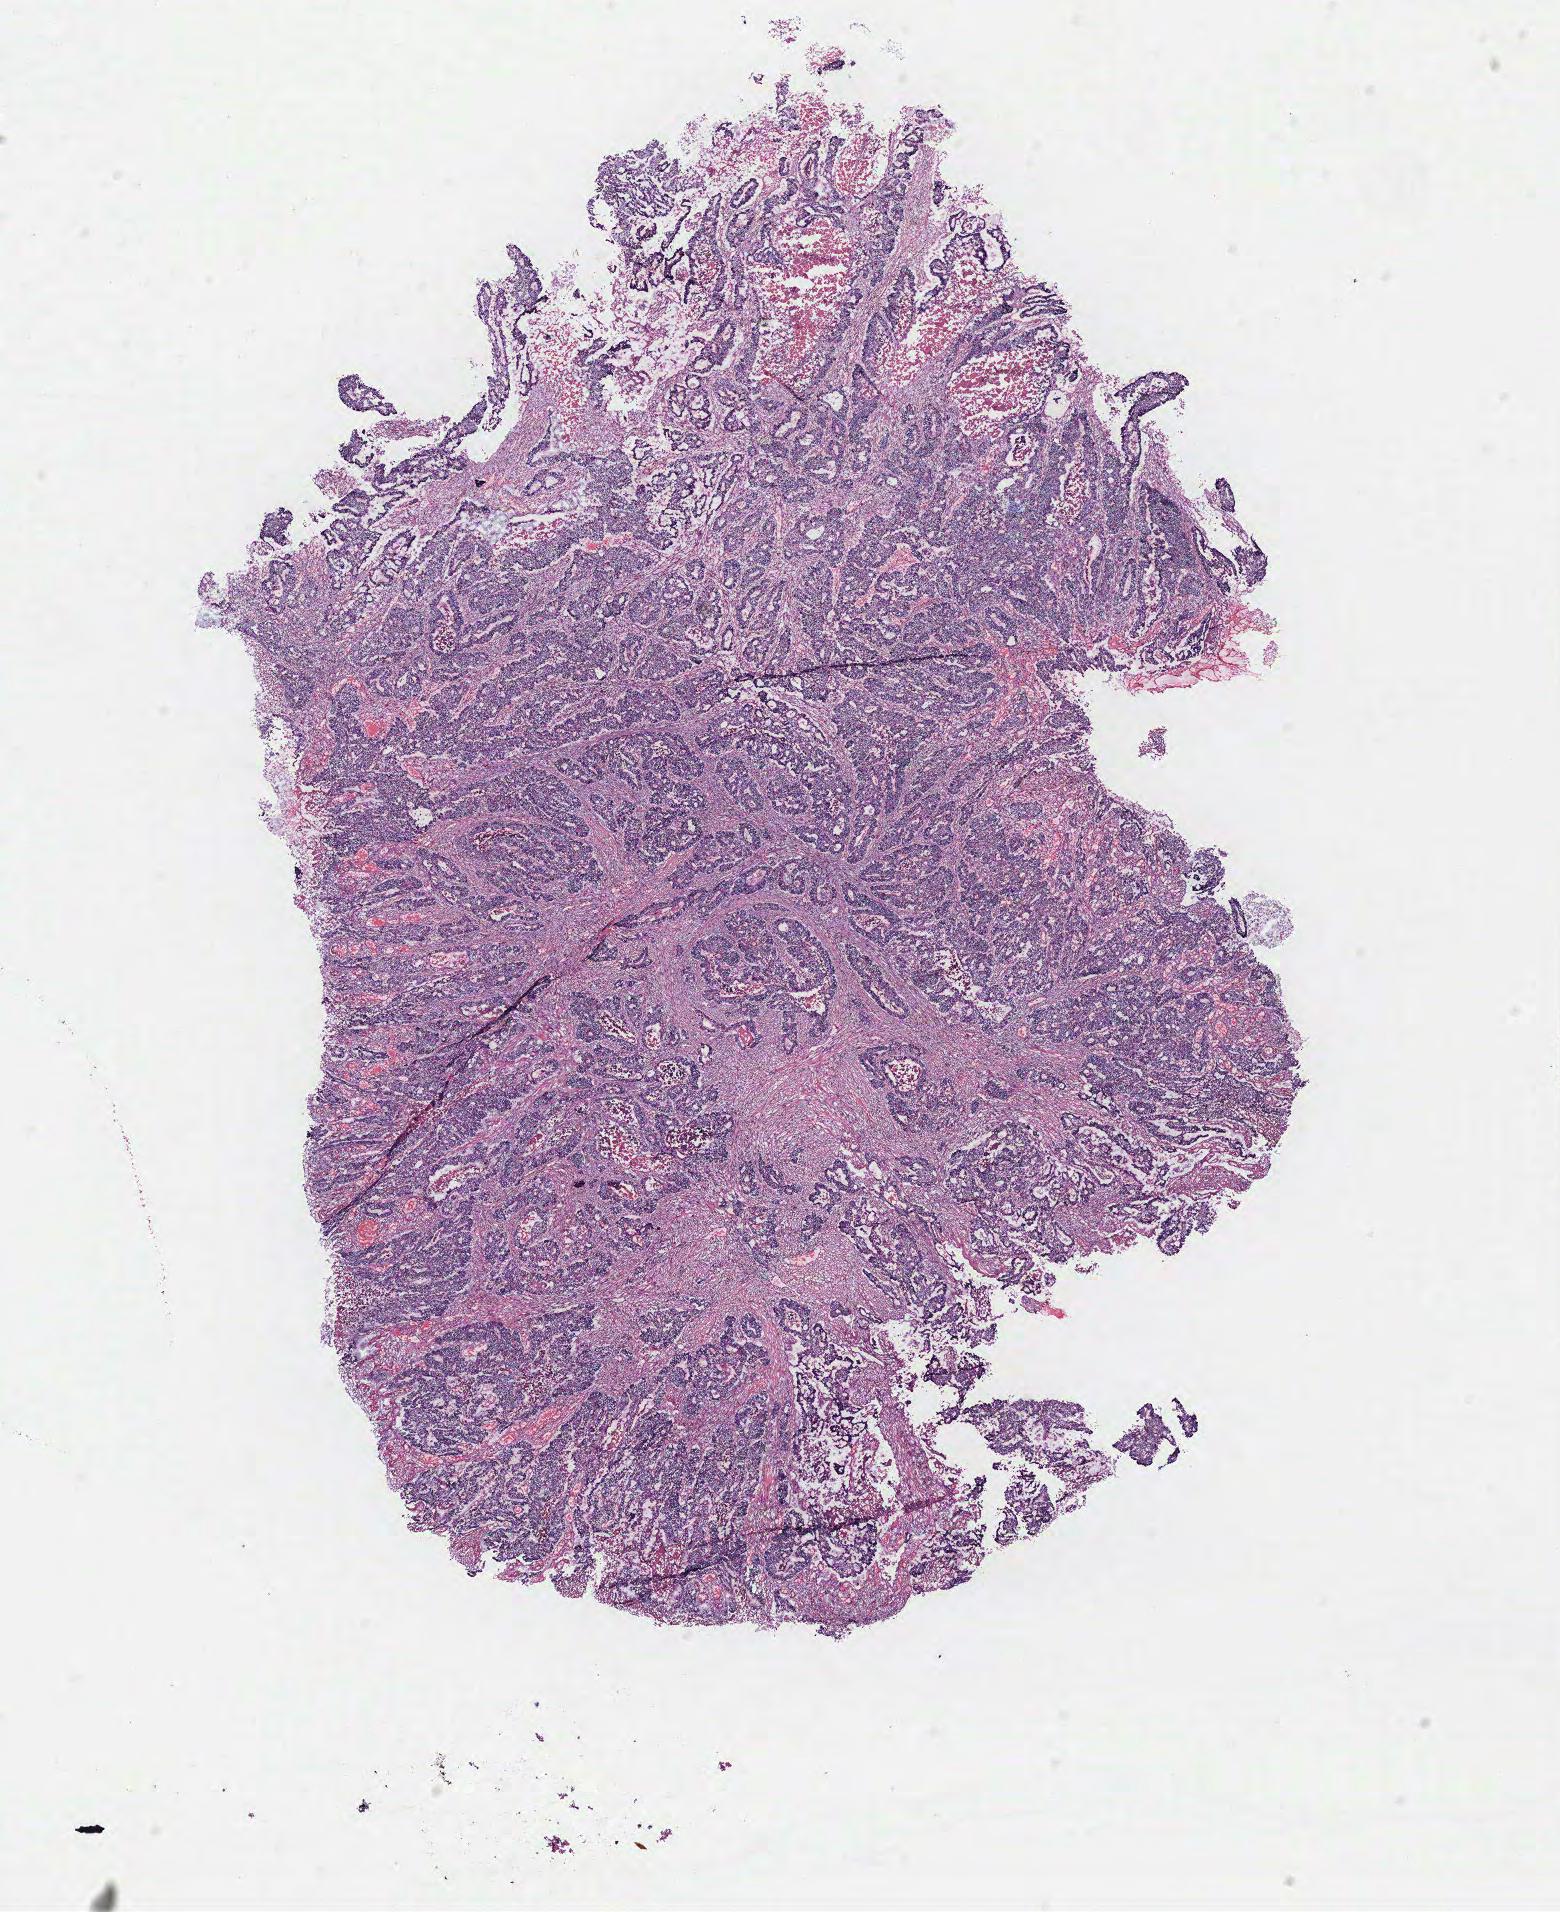
Digitized H&E-stained tissue section (whole slide) — whole scanned area (about 12.5 x 15.3 mm, from a 40x scan) shown as a low-resolution overview. Tumour tissue sample, colon. 50-year-old male patient.
Diagnosis: Adenocarcinoma, NOS. AJCC pathologic stage: IIIB. Primary tumour site (as recorded): colon.